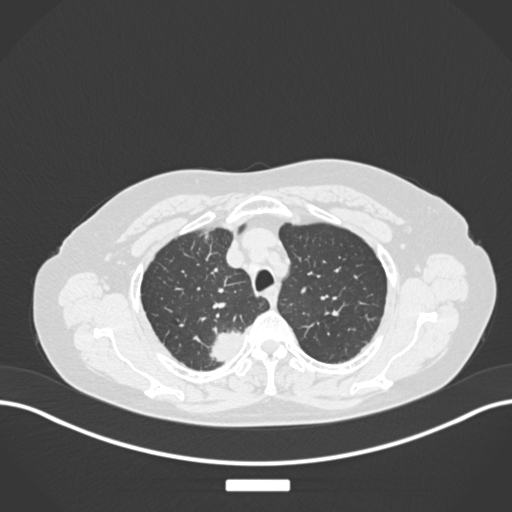
Chest CT, one axial slice. Position 209 of 237 along the scan axis. Reconstruction kernel B30f. 120 kVp. Lung window (W 1500 / L -600 HU). 1 mm slice thickness. 512 × 512 image matrix. Patient: female, 62 years. Case-level facts recorded for this patient, not image findings: clinical TNM (as recorded): T1c N1 M0.
Outlined on this slice (rectangle marked by the reading radiologist):
- lung tumour (recorded histology: squamous cell carcinoma): bounding box (x1, y1, x2, y2) in pixels: (207, 326, 247, 364)